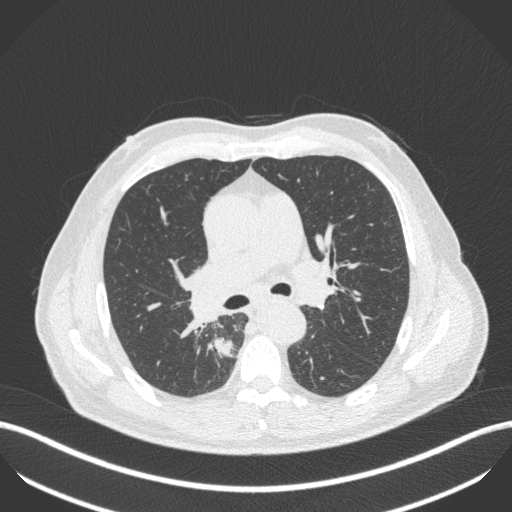
Chest CT, one axial slice; slice 284 of 451 in the series (ordered by position); lung window (W 1500 / L -600 HU); 1 mm slice thickness; 512 × 512 image matrix, field of view 400 × 400 mm. Patient: male, 61 years. From the clinical record (not read from this slice): clinical TNM (as recorded): T1 N0 M0; histopathological grade: G3.
Annotated regions visible in this slice (bounding box drawn by a radiologist):
- lung tumour (recorded histology: small cell carcinoma): bounding box (x1, y1, x2, y2) in pixels: (208, 332, 235, 360)